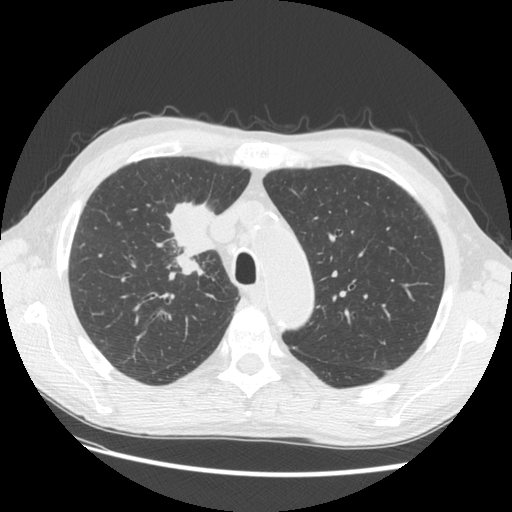
Chest CT (low-dose screening protocol), one axial image. Third annual screen. Lung window (W 1500 / L -600 HU). 2.5 mm slice thickness. Standard (soft-tissue) reconstruction kernel (STANDARD). 120 kVp. Slice 34 of 133 in the series. 512 × 512 image matrix. Male participant, aged 73 years at enrolment. Current smoker at enrolment.
Expert-annotated lung lesion, bounding box (x1, y1, x2, y2) in pixels: (142, 182, 233, 278). The screening reader recorded 4 non-calcified nodules or masses ≥4 mm on this exam (right upper lobe, right upper lobe, right upper lobe, left lower lobe); which of them this box marks is not recorded. Official screen result: positive, other. Lung cancer was diagnosed 48 days after this screen: squamous cell carcinoma, NOS, right upper lobe, poorly differentiated (G3), stage IIIB (AJCC 6th edition), 56 mm at pathology.